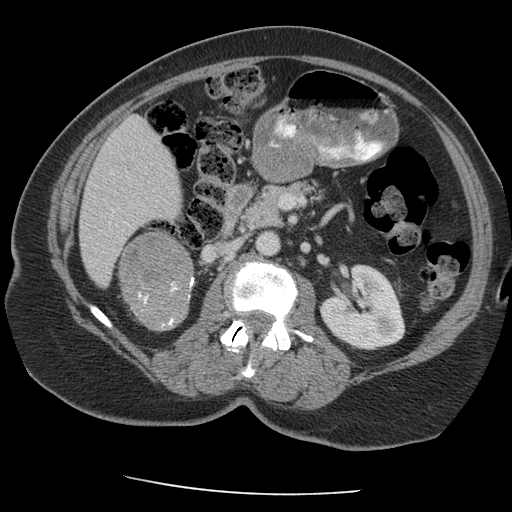
Contrast-enhanced abdominal CT, one axial slice; position 110 of 163 along the scan axis; 140 kVp; intravenous contrast given; soft-tissue window (W 400 / L 40 HU); 2.5 mm slice thickness; 512 × 512 image matrix, field of view 360 × 360 mm. Patient: female, 70 years. From the clinical record (not read from this slice): diagnosis: adrenocortical carcinoma; tumour side: right adrenal; tumour size at pathology: 9.5 cm; Ki-67 index: 5 %; stage (as recorded): 2.
Structures marked on this image (semi-automatically segmented with operator editing):
- mass: bounding box [x1, y1, x2, y2] px = [120, 234, 192, 329]